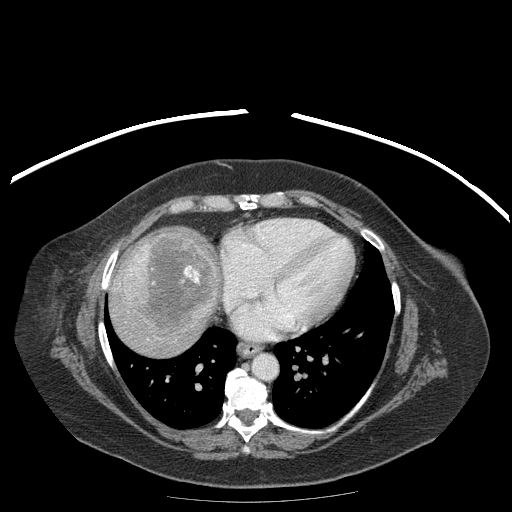
Contrast-enhanced abdominal CT (liver protocol), one axial slice. Slice 171 of 204 in the series (ordered by position). Soft-tissue window (W 400 / L 40 HU). 2.5 mm slice thickness. 512 × 512 image matrix, field of view 440 × 440 mm. Case-level facts recorded for this patient, not image findings: diagnosis: hepatocellular carcinoma (patient treated with transarterial chemoembolisation; whether this scan precedes or follows treatment is not stated here); TNM stage (as recorded): Stage-IIIB; Child-Pugh class: A; tumour differentiation: well differentiated; tumour nodularity: uninodular.
Outlined on this slice (semi-automatically segmented with operator editing):
- liver parenchyma outside the tumour (the mass and vessels are separate outlines, so this box may not span the whole liver): bounding box (x1, y1, x2, y2) in pixels: (110, 228, 218, 354)
- mass: (117, 234, 217, 332)